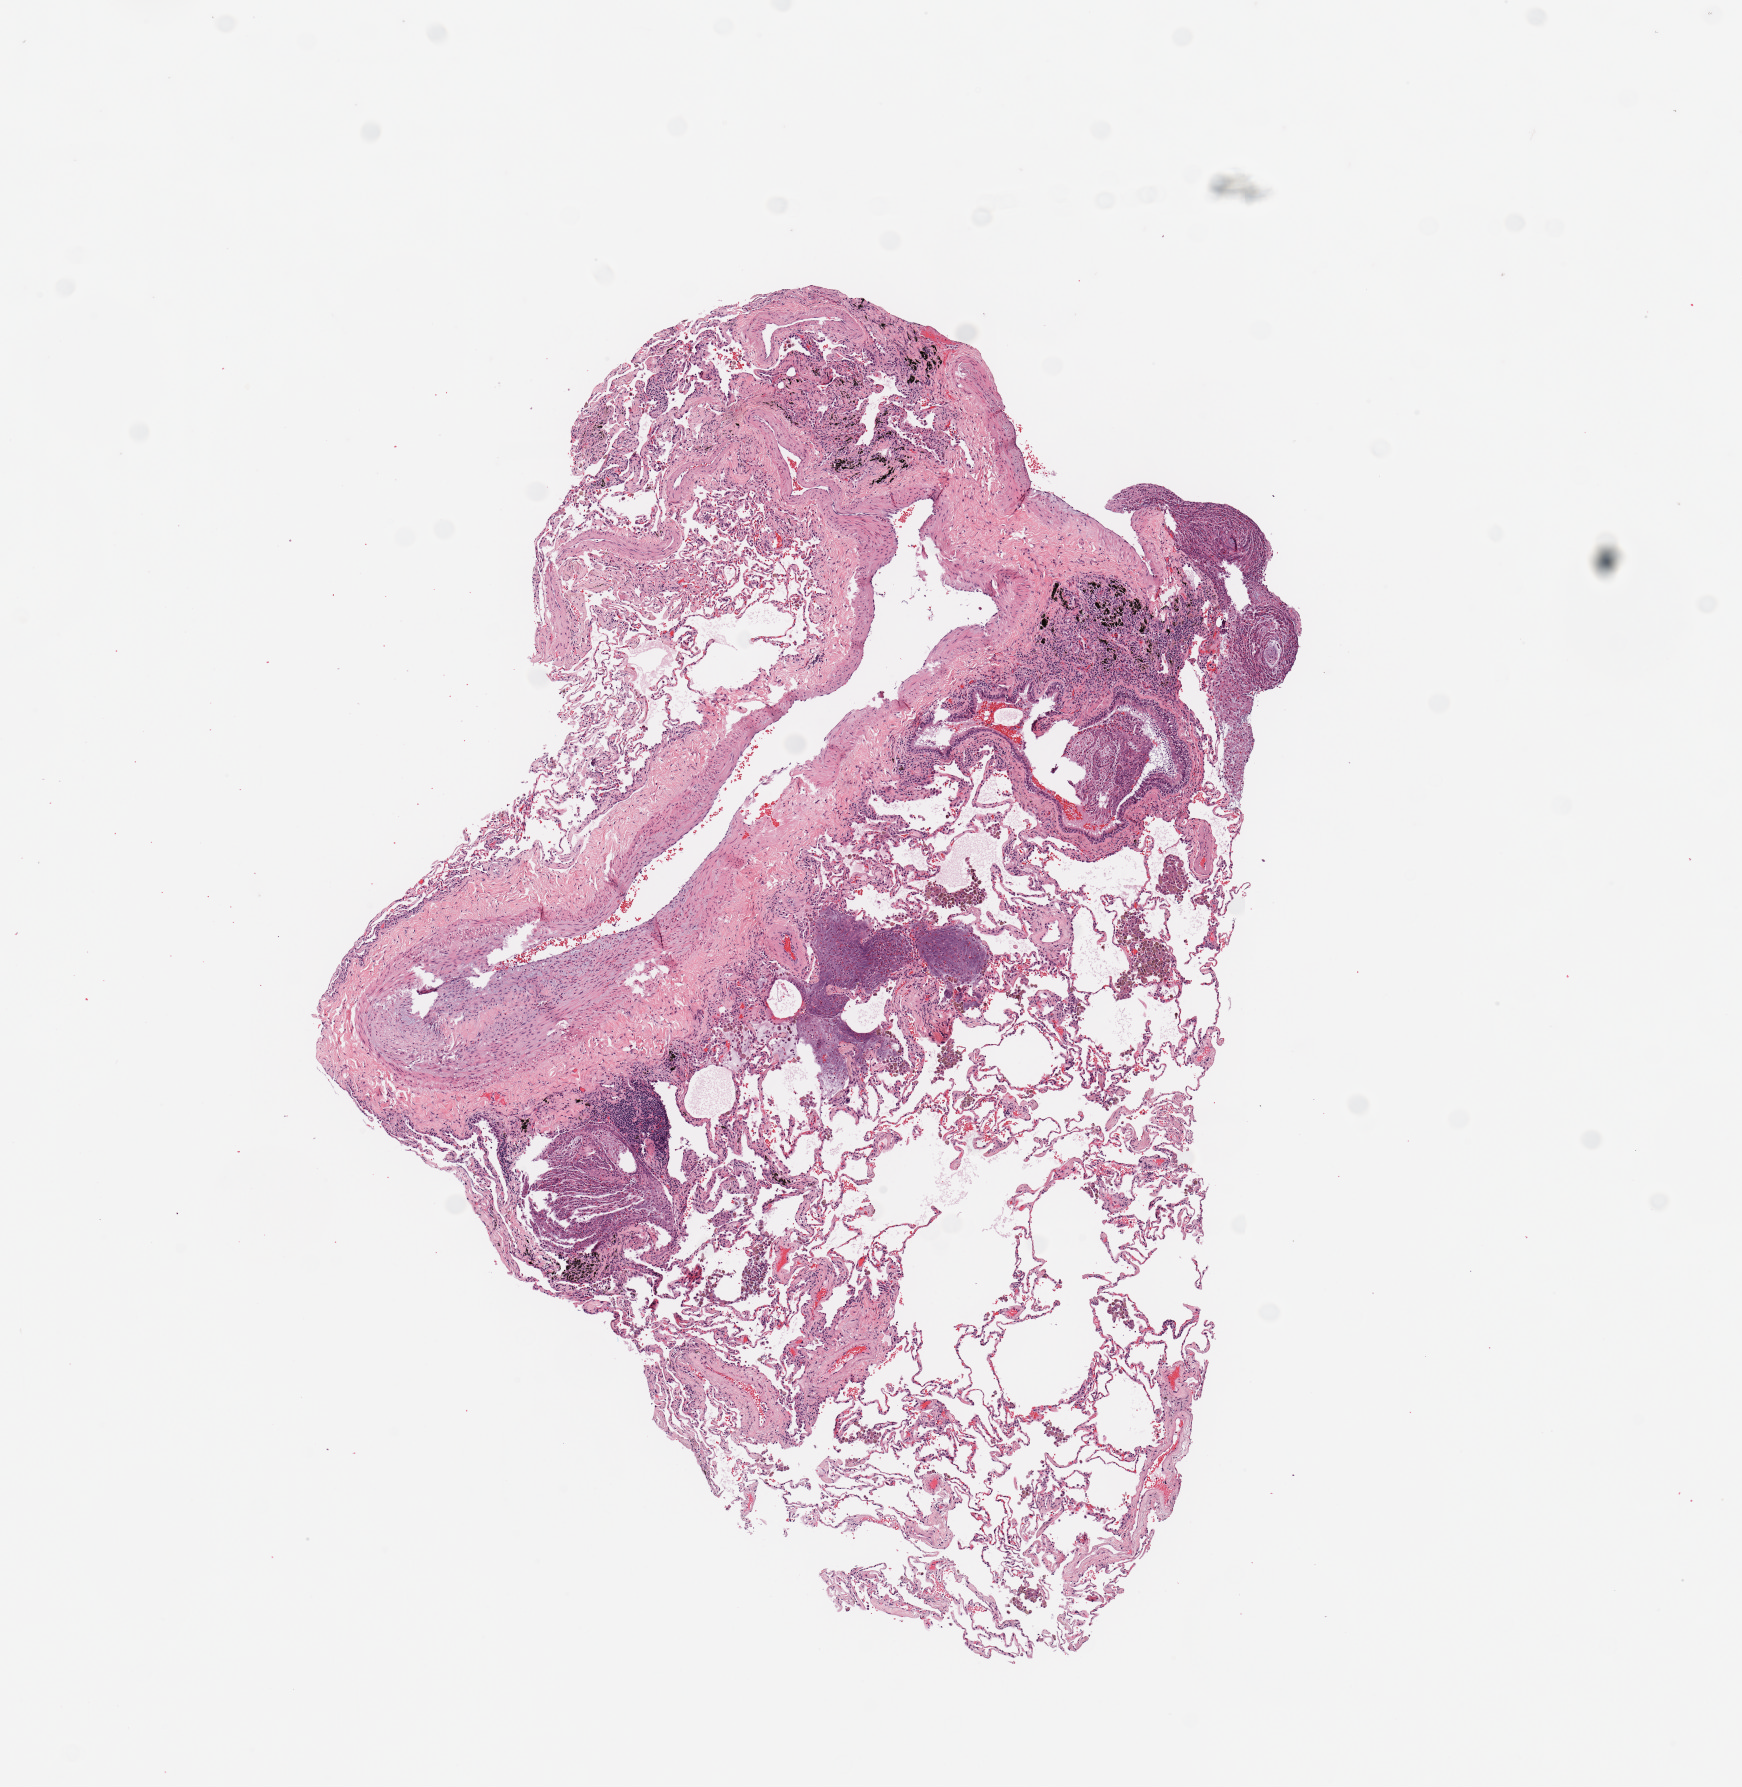
Hematoxylin and eosin (H&E) stained whole-slide image, a low-resolution overview of the entire scanned area, about 6.9 x 7.1 mm (acquisition: 20x scan), lung, normal (non-tumour) tissue. Male, 69 y/o.
- this section: normal (non-tumour) tissue from the same patient
- patient diagnosis: Squamous cell carcinoma, NOS